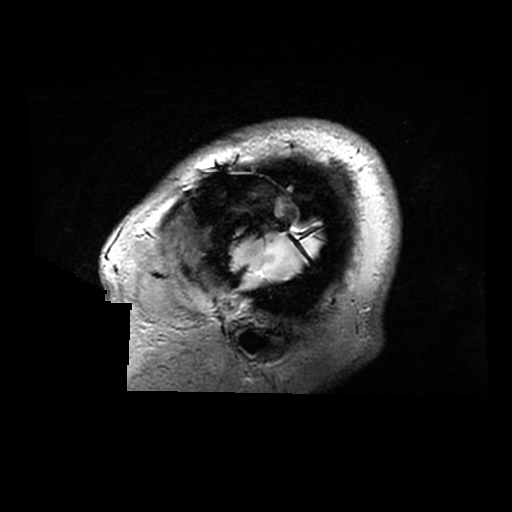
Brain MRI from a brain-tumour surgery series, one sagittal slice. Slice 261 of 320 in the series (ordered by position). 512 × 512 image matrix. Case-level facts recorded for this patient, not image findings: histopathology: Astrocytoma; WHO grade: 2; IDH mutation: yes.
Outlined on this slice (manually delineated by an expert):
- tumour: bounding box (x1, y1, x2, y2) in pixels: (232, 235, 318, 280)